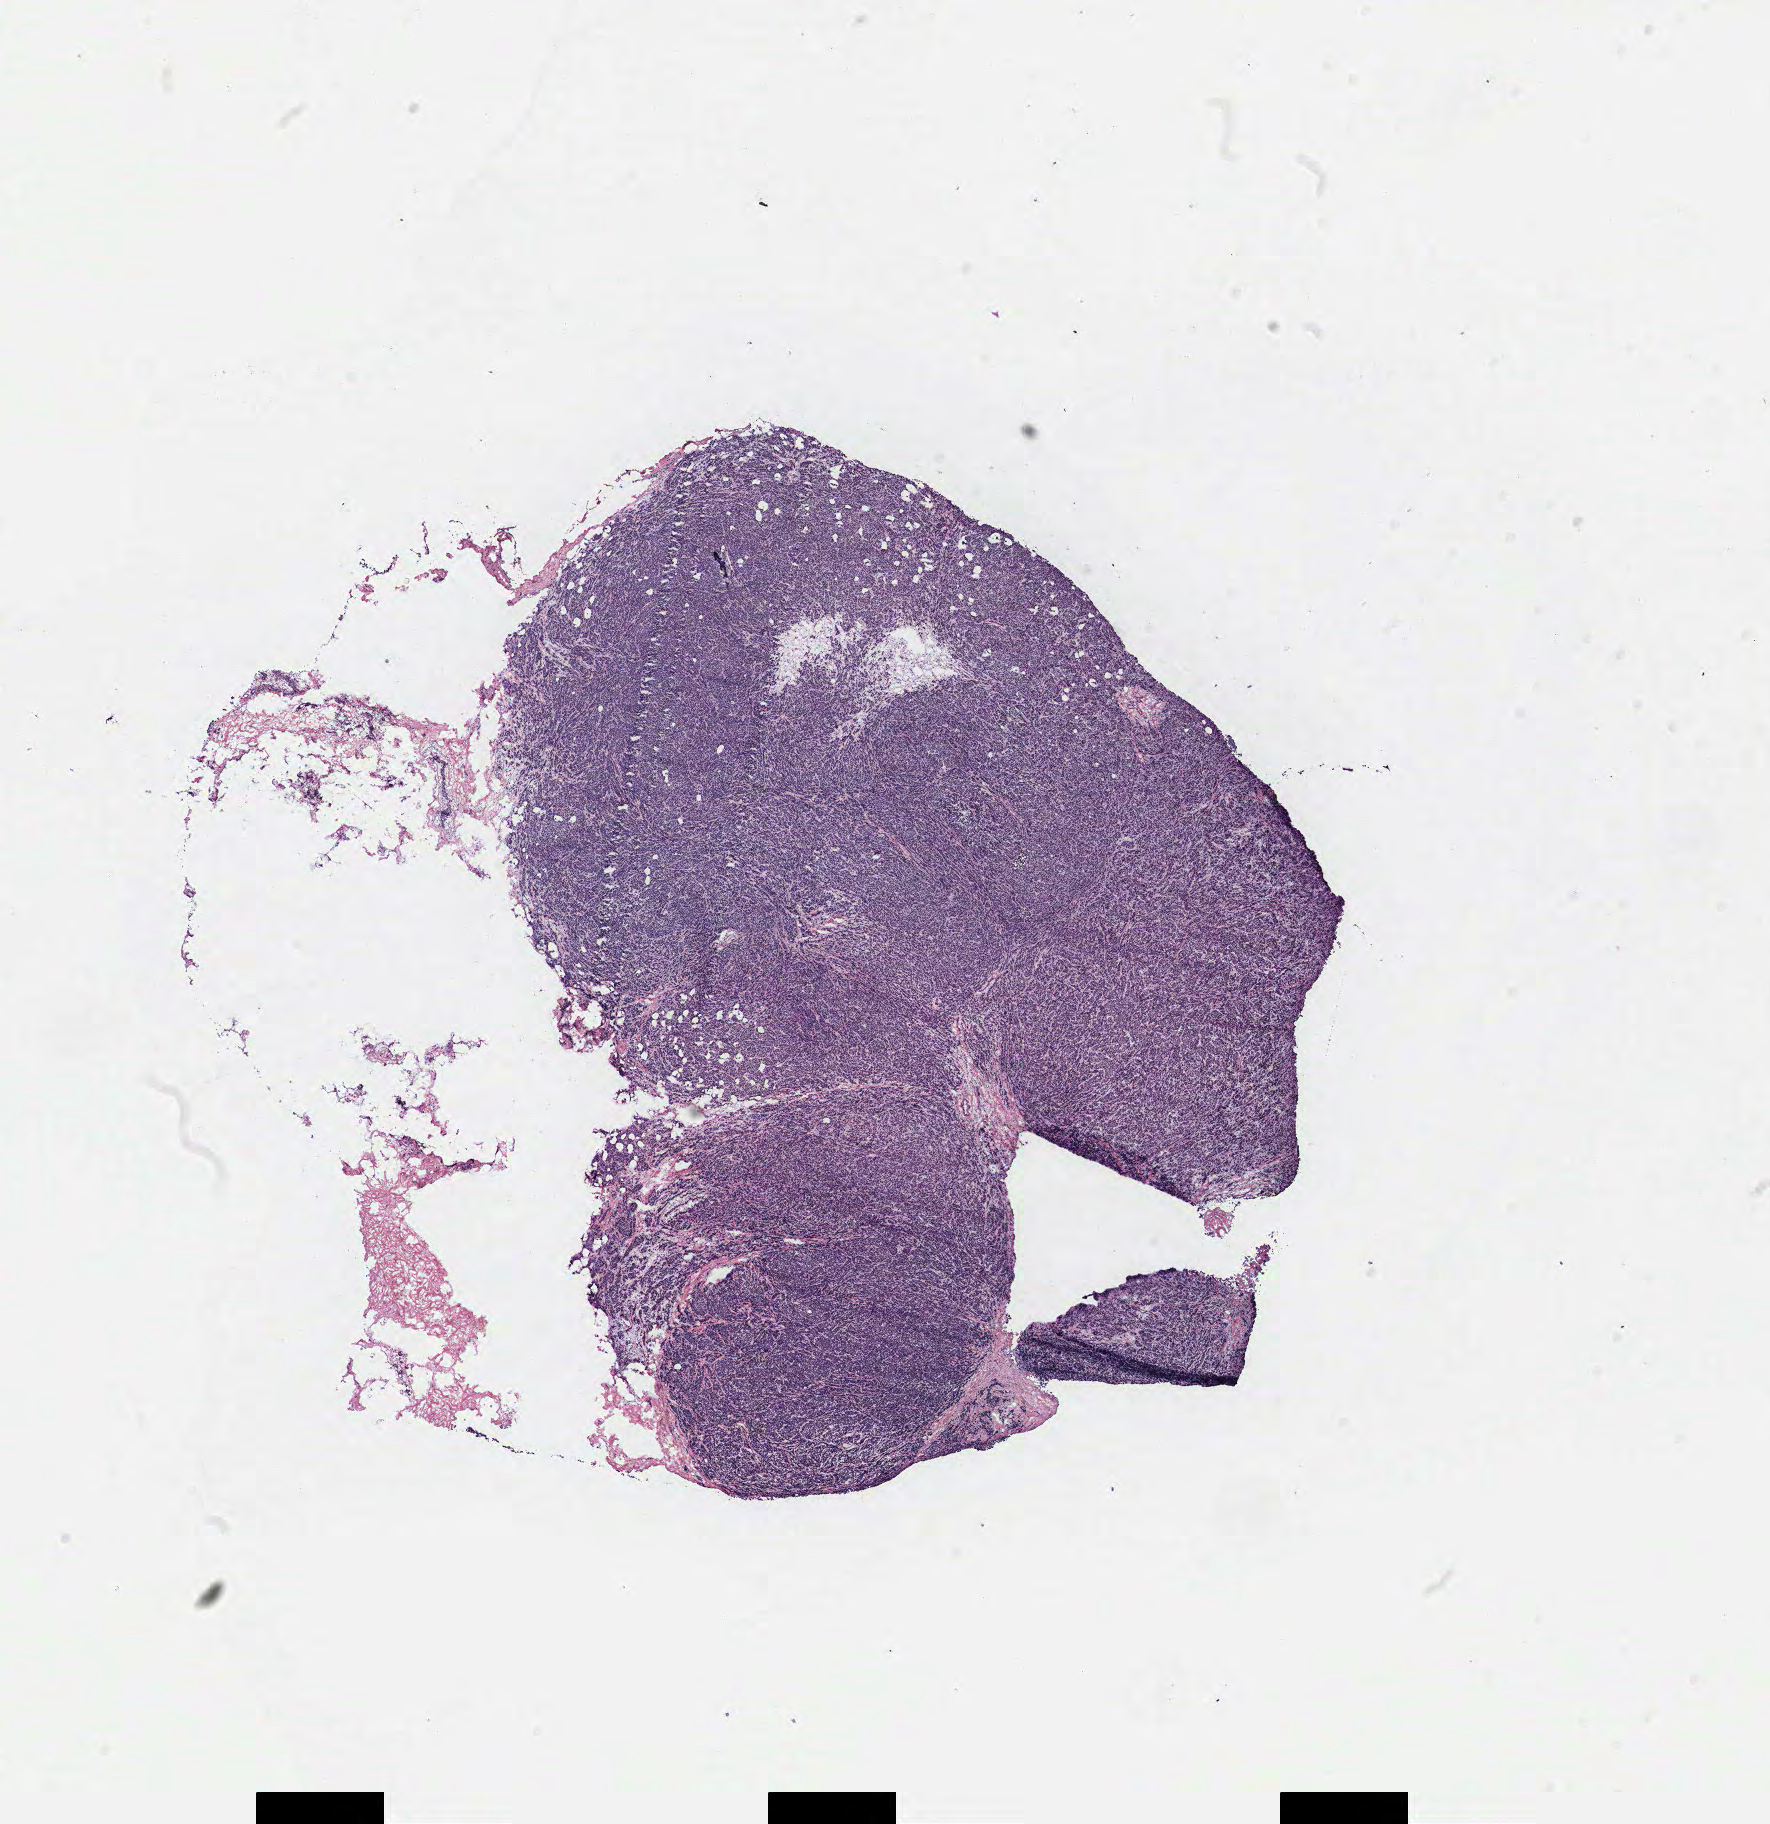
Whole-slide histology image, H&E — a low-resolution overview of the entire scanned area, about 14.2 x 14.6 mm. Tumour tissue sample, breast. Patient: female, age 78 years.
Diagnosis: Infiltrating duct carcinoma, NOS. AJCC pathologic stage: IIA.